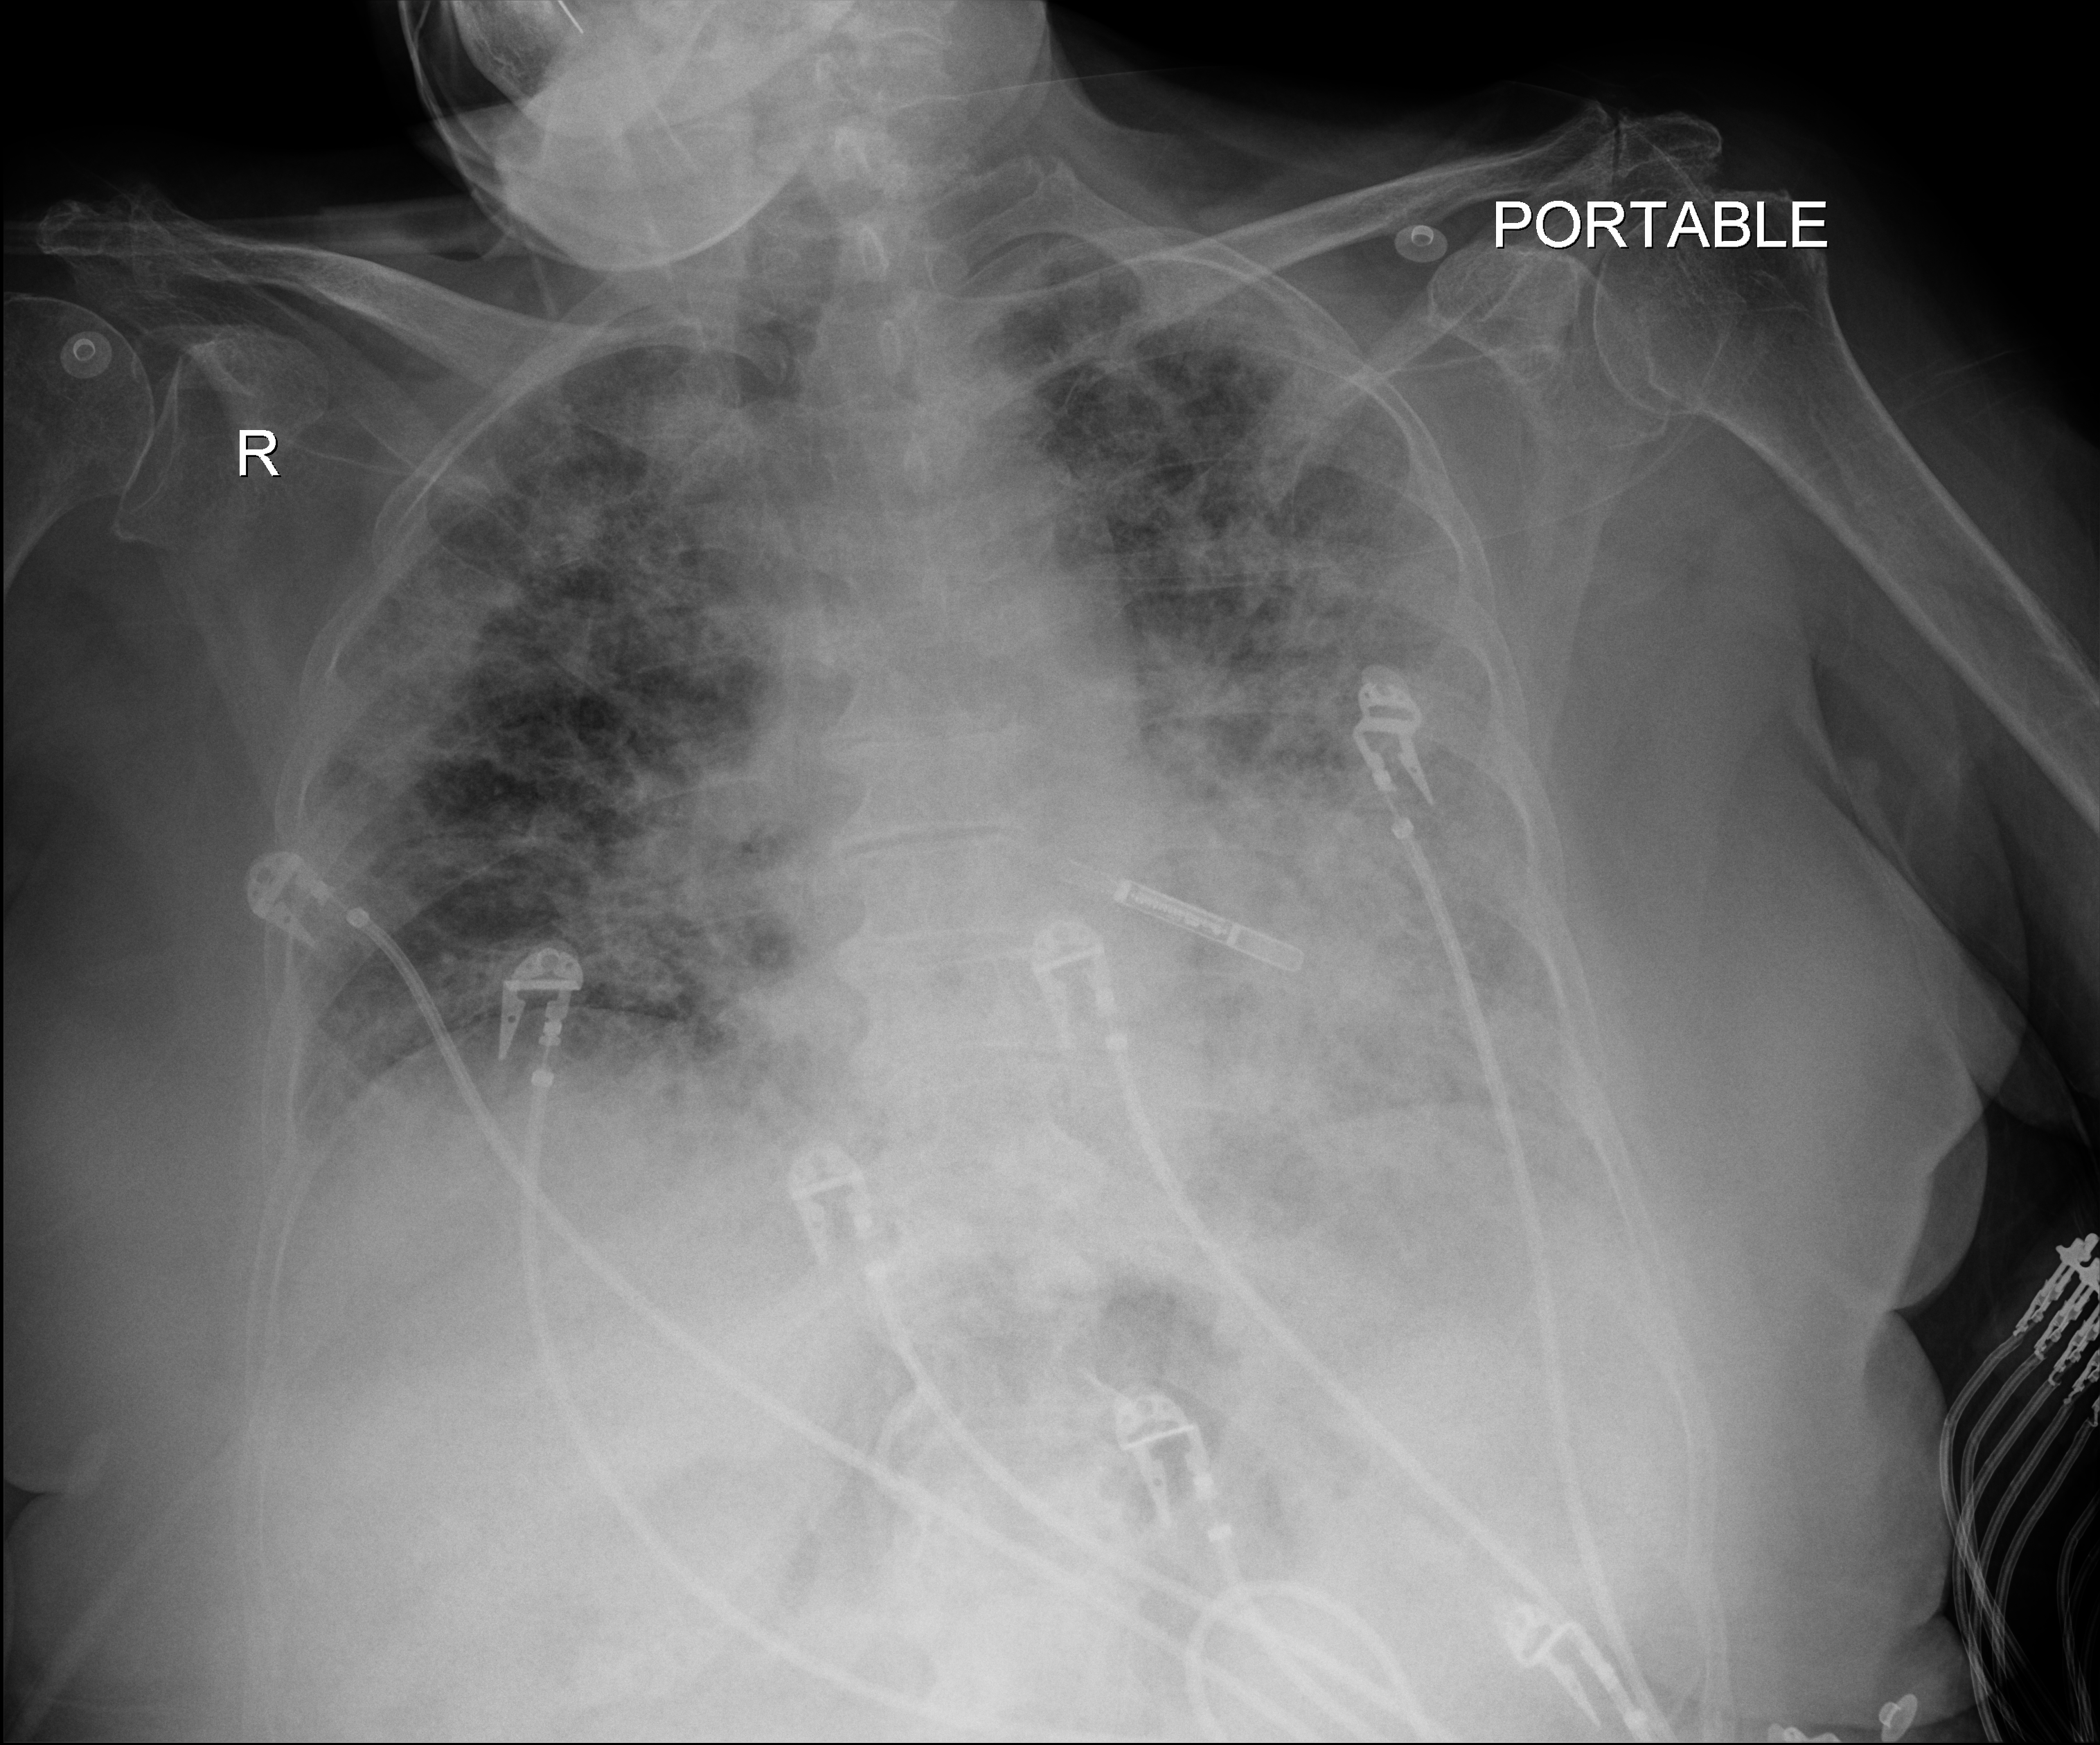
Chest radiograph (digital radiography), anteroposterior (AP) projection. Patient hospitalised with COVID-19; female, aged 75–90 years.
From the hospital-stay record, not from the radiograph (when in the stay this image was taken is not recorded):
- mechanically ventilated during this hospital stay: no
- length of hospital stay: 10 days